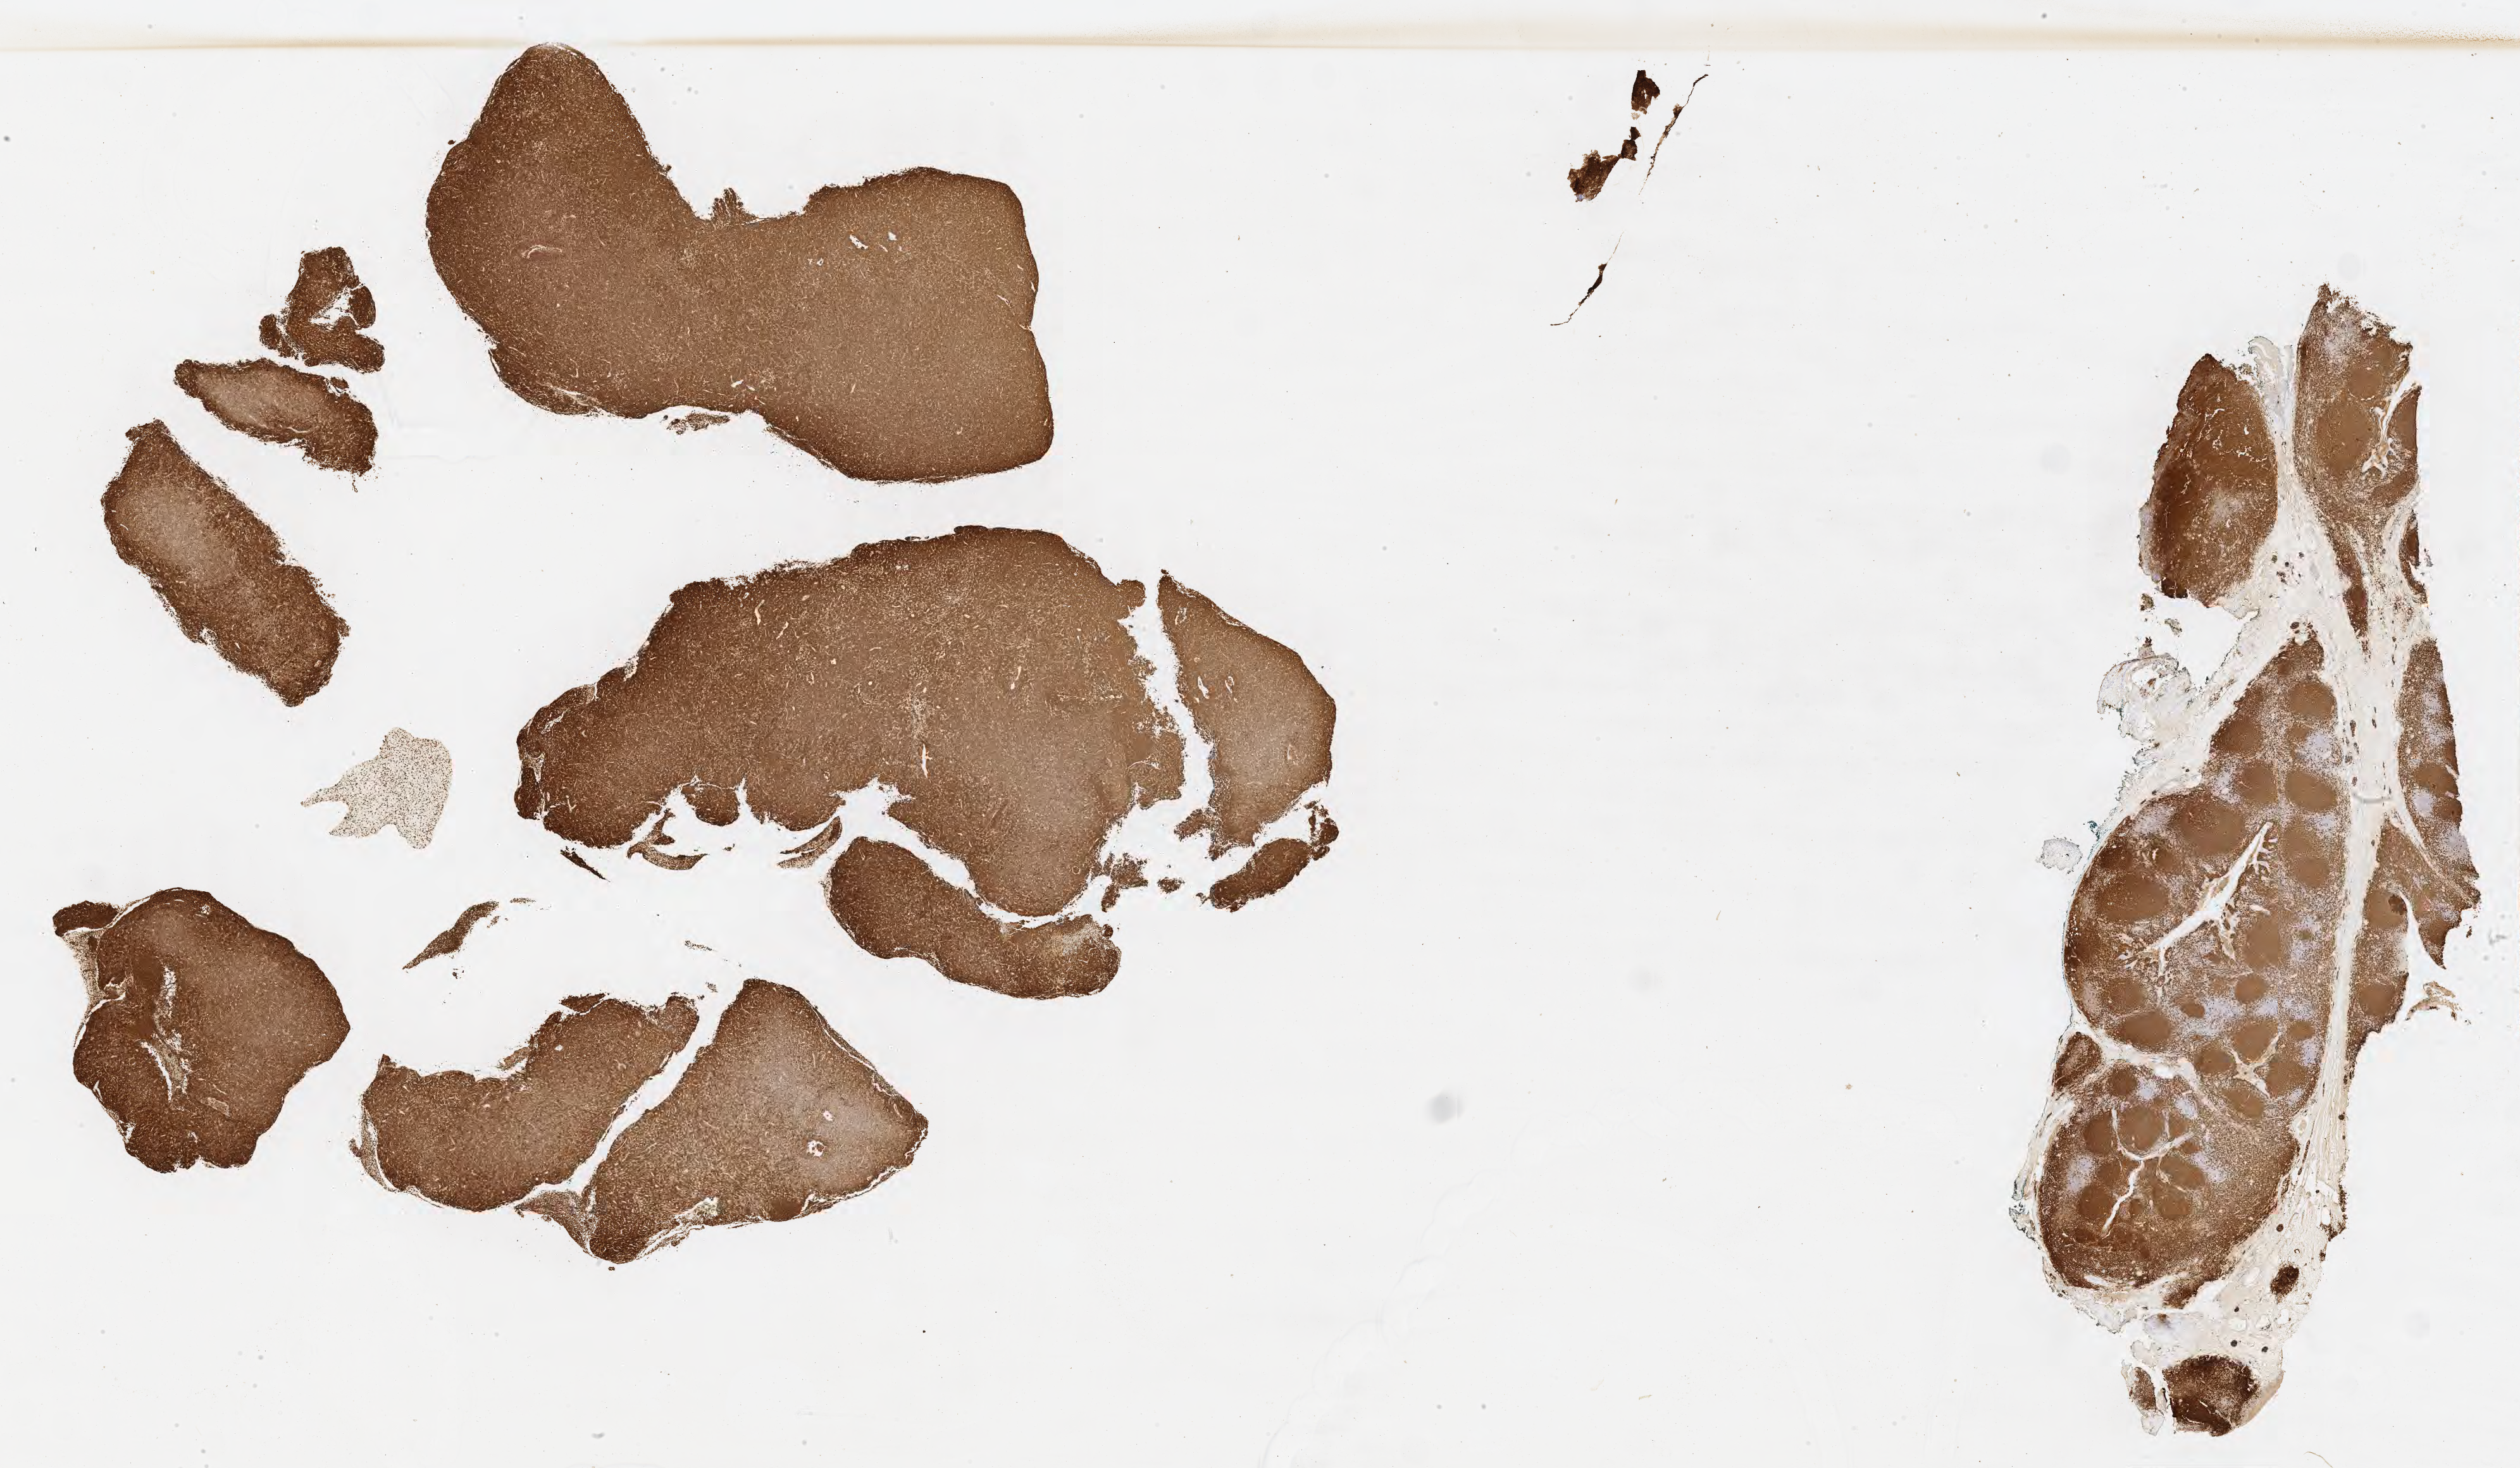
Whole-slide image, immunohistochemical stain for CD20 — whole scanned area (about 32.2 x 18.8 mm) shown as a low-resolution overview, tumor tissue, site: soft tissue. Female patient; age at initial diagnosis 9 years.
Diagnosis: Burkitt lymphoma, NOS.